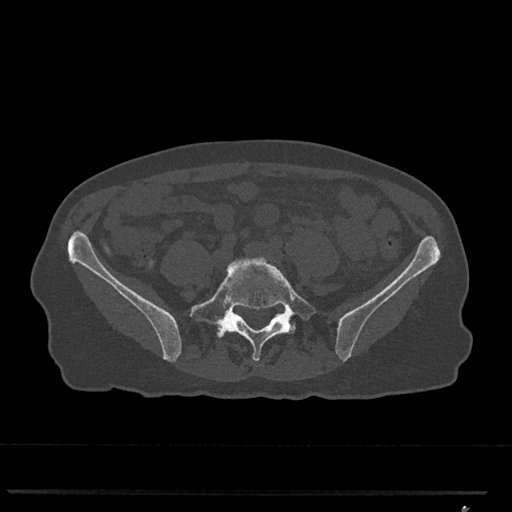
CT including the spine, one axial slice. Position 152 of 793 along the scan axis. Reconstruction kernel Br40s/3. 120 kVp. Bone window (W 1800 / L 400 HU). 0.5 mm slice thickness. 512 × 512 image matrix, field of view 380 × 380 mm. Female patient, age 62 years. Case-level facts recorded for this patient, not image findings: primary cancer: renal.
Outlined on this slice (semi-automatic segmentation, software-assisted and operator-edited):
- L5 vertebra: box from (x=190, y=257) to (x=316, y=361) px